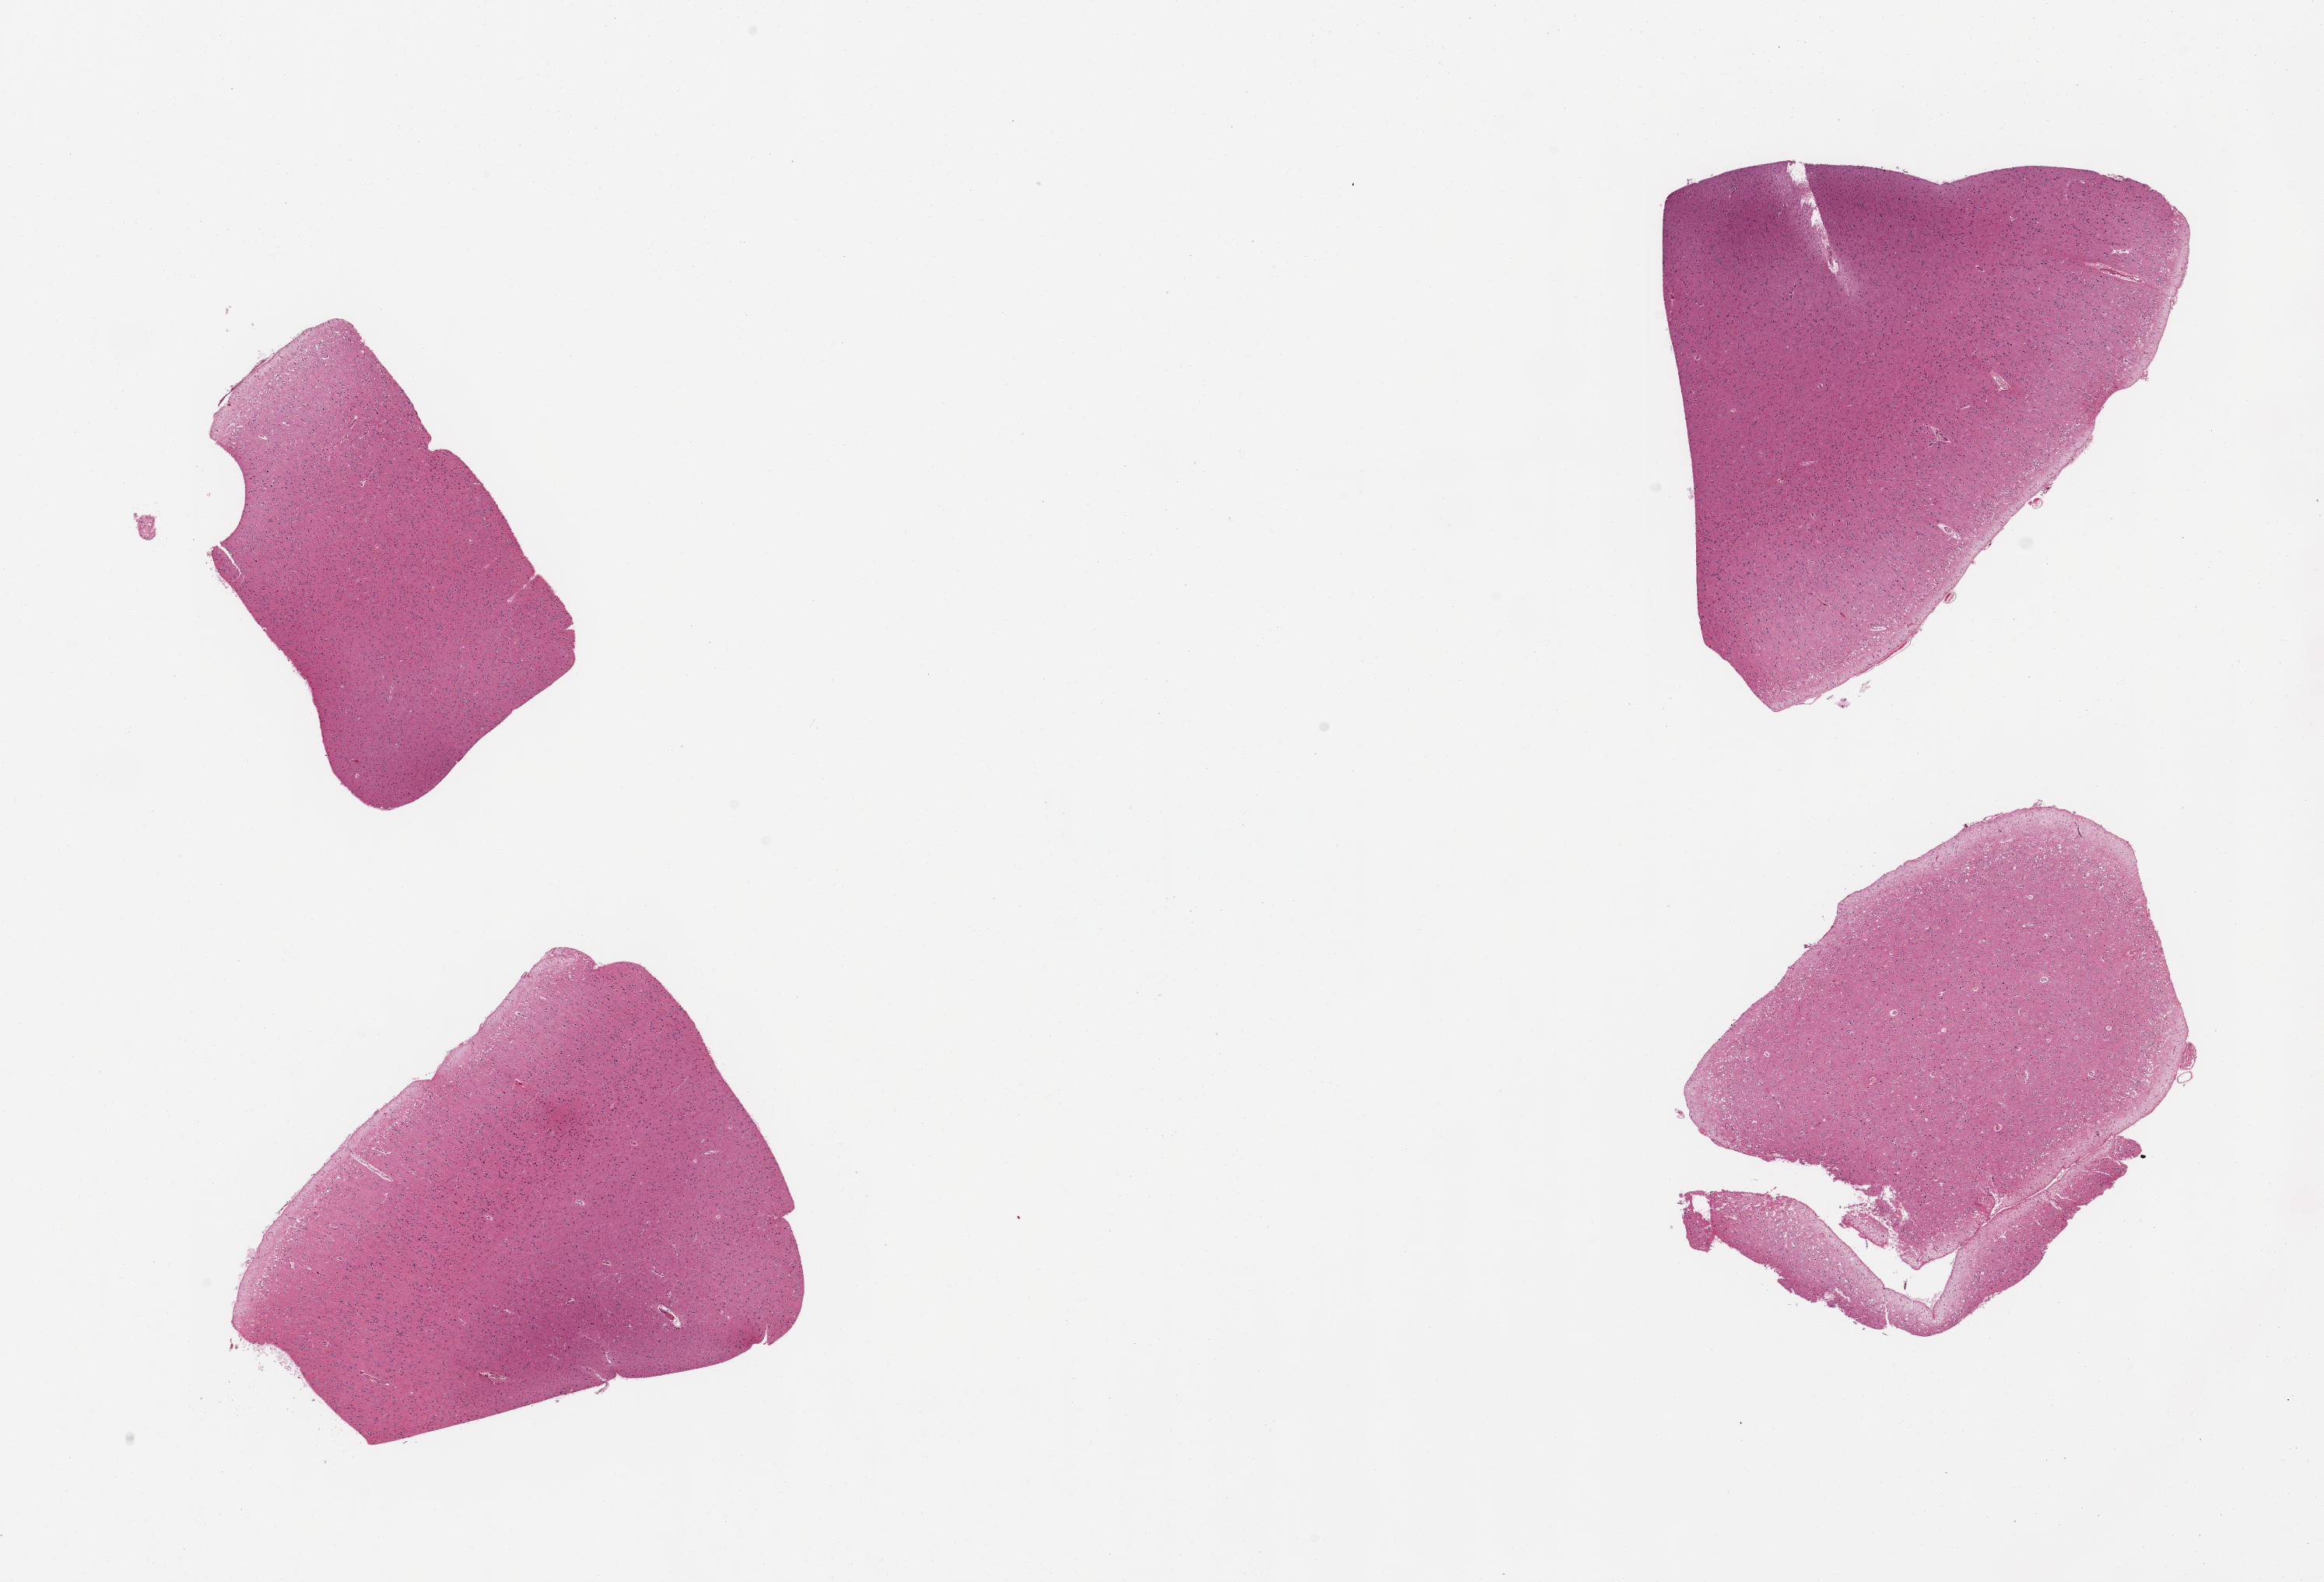
Digitized hematoxylin and eosin (H&E)-stained section, brightfield — shown as a low-resolution overview of the whole scanned area (about 23.6 x 16.1 mm). PAXgene-fixed paraffin-embedded (PFPE) section. Sampled site (target tissue): cerebral cortex. Tissue donor sample.
Review note (as recorded): 4 pieces; mild to moderate autolysis.